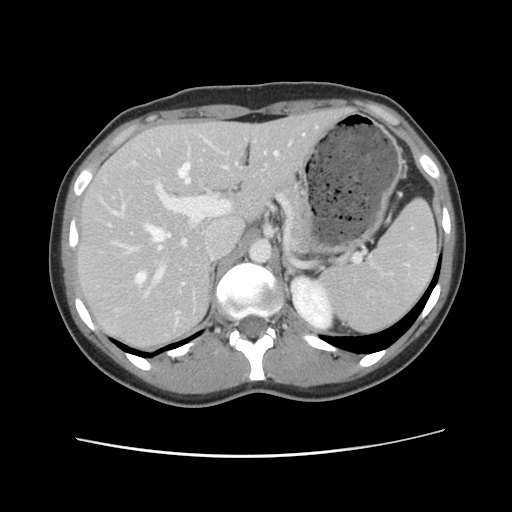
Contrast-enhanced abdominal CT, one axial slice; position 72 of 134 along the scan axis; soft-tissue window (W 400 / L 40 HU); 2.5 mm slice thickness; 512 × 512 image matrix, field of view 339 × 339 mm. Female patient, age 33 years. From the clinical record (not read from this slice): diagnosis: colorectal cancer liver metastases, imaged before liver resection; multiple liver metastases: yes; largest metastasis: 4.5 cm; chemotherapy before resection: no.
Structures marked on this image (outlined manually by an expert reader):
- hepatic veins: bounding box [x1, y1, x2, y2] px = [116, 152, 279, 295]
- liver: [78, 109, 345, 351]
- planned liver remnant (the part of the liver to remain after resection): [78, 110, 344, 351]
- portal vein (with intrahepatic branches): [151, 139, 294, 277]